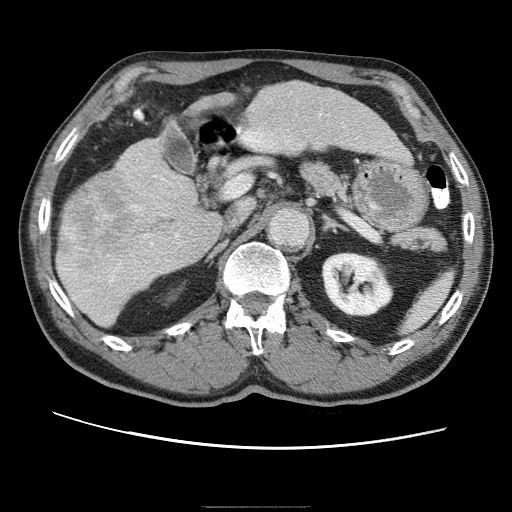
Contrast-enhanced abdominal CT (liver protocol), one axial slice; position 26 of 75 along the scan axis; reconstruction kernel STANDARD; 120 kVp; one of 2 acquisitions stored at this slice position; soft-tissue window (W 400 / L 40 HU); 2.5 mm slice thickness; 512 × 512 image matrix, field of view 360 × 360 mm. Case-level facts recorded for this patient, not image findings: diagnosis: hepatocellular carcinoma (patient treated with transarterial chemoembolisation; whether this scan precedes or follows treatment is not stated here); TNM stage (as recorded): Stage-II; Child-Pugh class: A; tumour differentiation: well differentiated; tumour nodularity: multinodular.
Annotated regions visible in this slice (semi-automatically segmented with operator editing):
- liver parenchyma outside the tumour (the mass and vessels are separate outlines, so this box may not span the whole liver): bounding box <56,84,404,324> (left, top, right, bottom; pixels)
- mass: <81,210,157,248>
- liver vessels: <61,156,204,285>